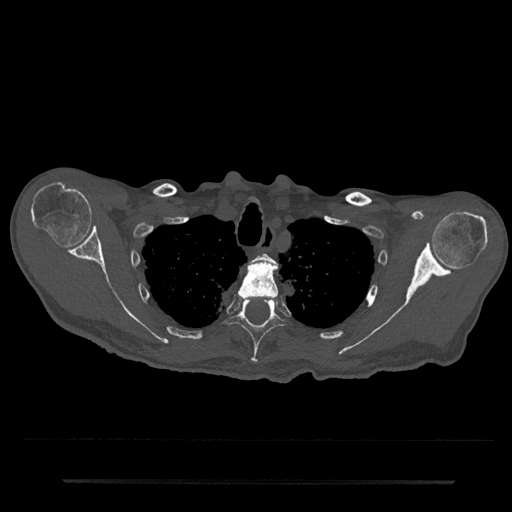
CT including the spine, one axial slice. Slice 635 of 797 in the series (ordered by position). Reconstruction kernel Br40s/3. Bone window (W 1800 / L 400 HU). 0.5 mm slice thickness. 512 × 512 image matrix. Male patient, age 74 years. From the clinical record (not read from this slice): primary cancer: prostate.
Annotated regions visible in this slice (semi-automatic segmentation, software-assisted and operator-edited):
- T2 vertebra: bounding box <254,253,274,262> (left, top, right, bottom; pixels)
- T3 vertebra: <238,260,279,297>
- T4 vertebra: <227,297,285,364>